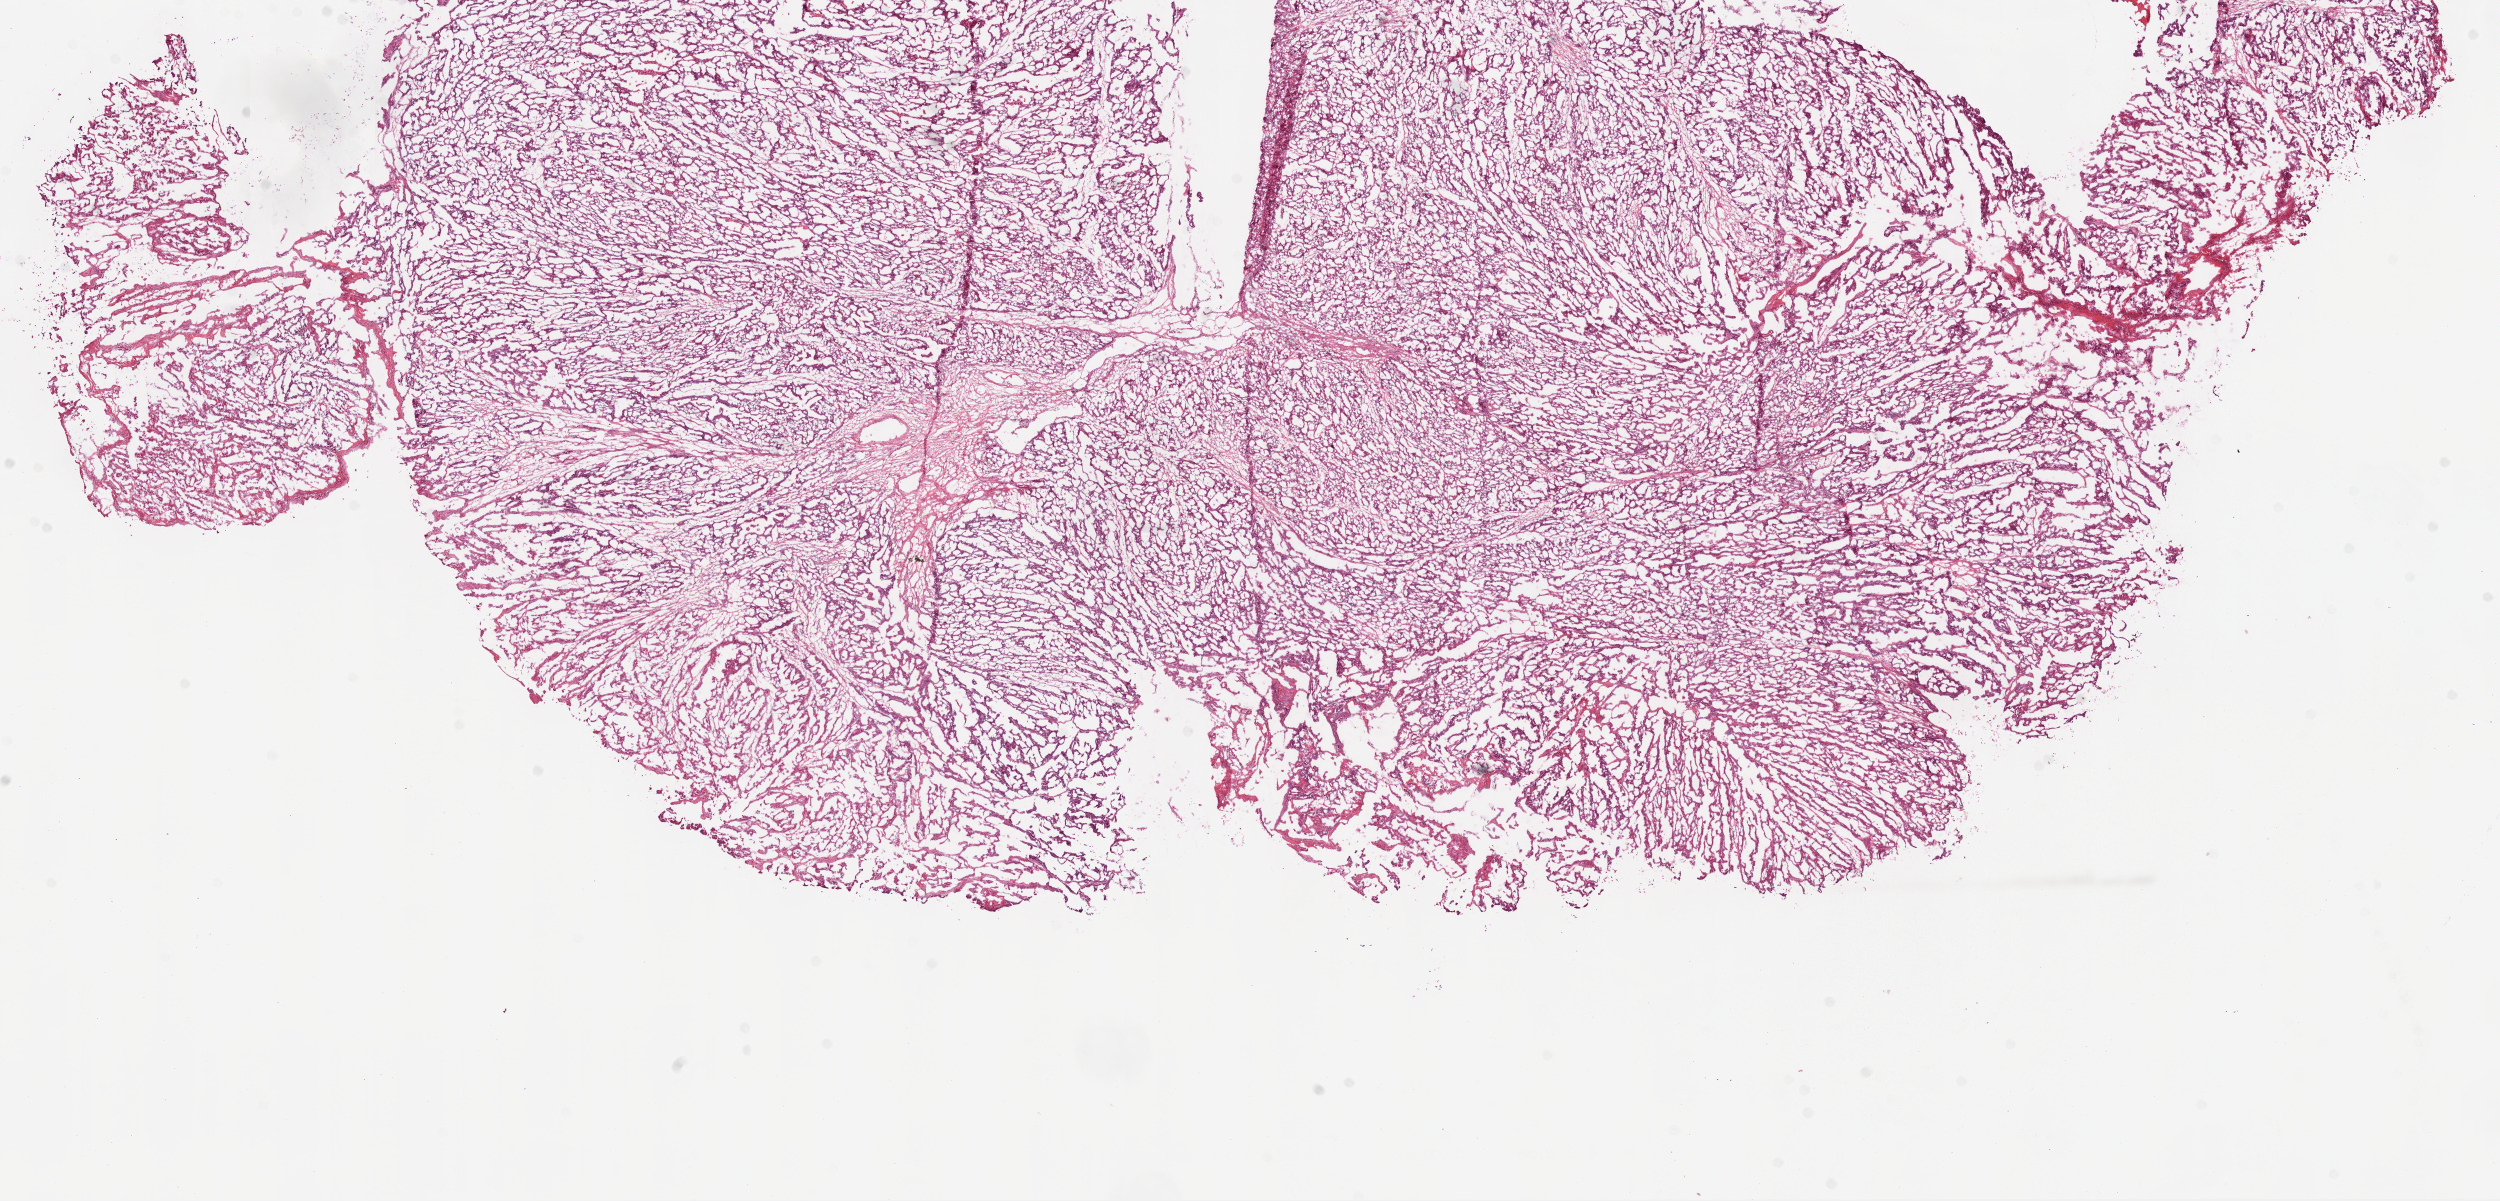
Hematoxylin and eosin (H&E) stained whole-slide image, low-resolution overview of the scanned area, about 20.1 x 9.6 mm (slide scanned at 20x), frozen section from the bottom of the tissue portion, colon, primary tumour sample. Female patient; age at initial diagnosis 71 years. Slide review estimates, as recorded: tumour cells 95%, tumour nuclei 80%.
Diagnosis: Adenocarcinoma, NOS (cecum).